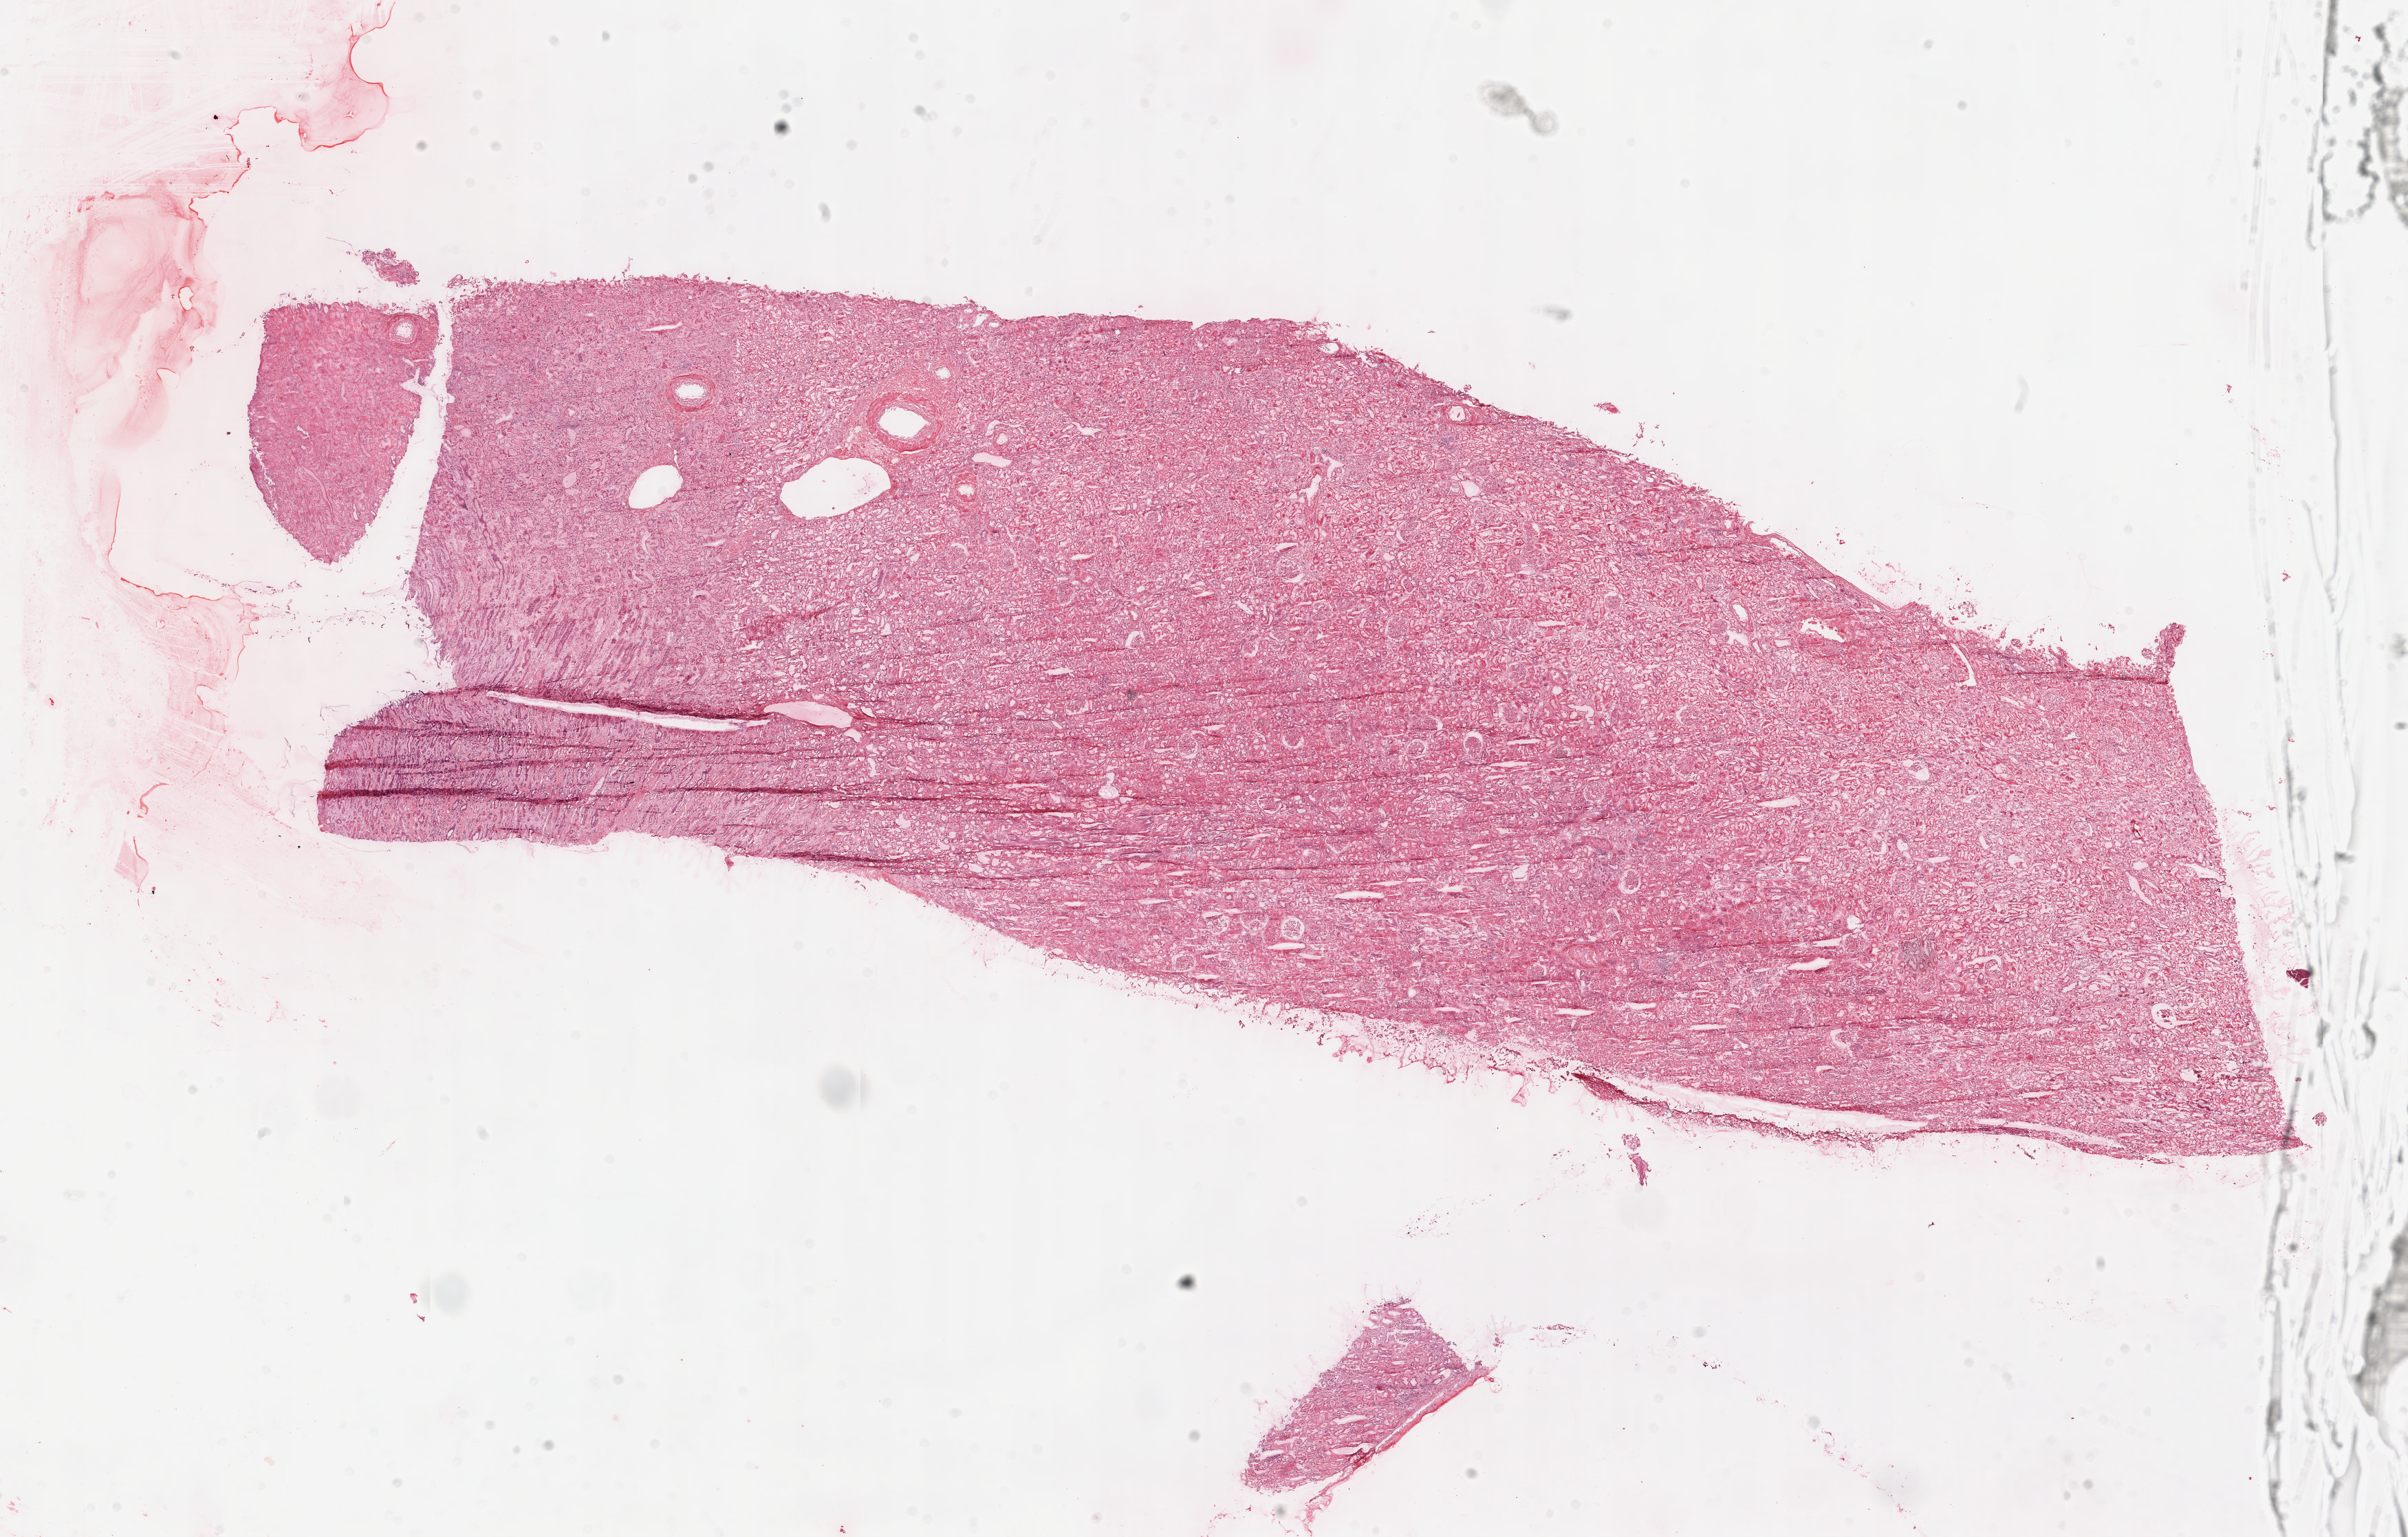
Whole-slide histology image, H&E-stained, whole scanned area (about 27.8 x 17.7 mm) shown as a low-resolution overview. Frozen section from the top of the tissue portion. Sample: solid tissue normal (non-tumour tissue), kidney. Male patient; age at initial diagnosis 63 years.
This section: solid tissue normal sample (biorepository sample class). Patient diagnosis: Clear cell adenocarcinoma, NOS.